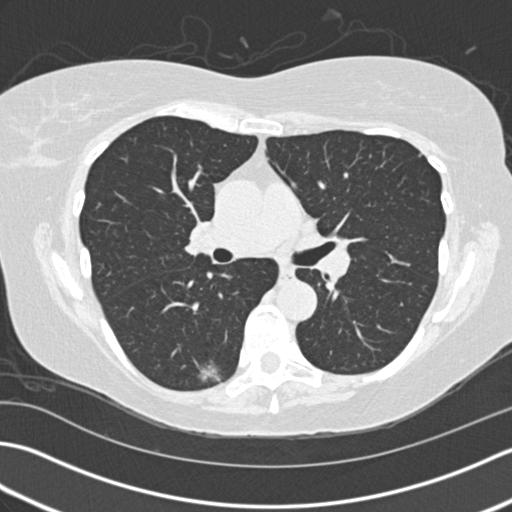
Low-dose screening chest CT, one axial slice. Slice 89 of 159 in the series (ordered by position). Lung window (W 1500 / L -600 HU). 2 mm slice thickness. 512 × 512 image matrix, field of view 350 × 350 mm.
Outlined on this slice (manually delineated by an expert):
- lesion 1 (tumor, lower lobe of right lung): box from (x=200, y=365) to (x=220, y=381) px